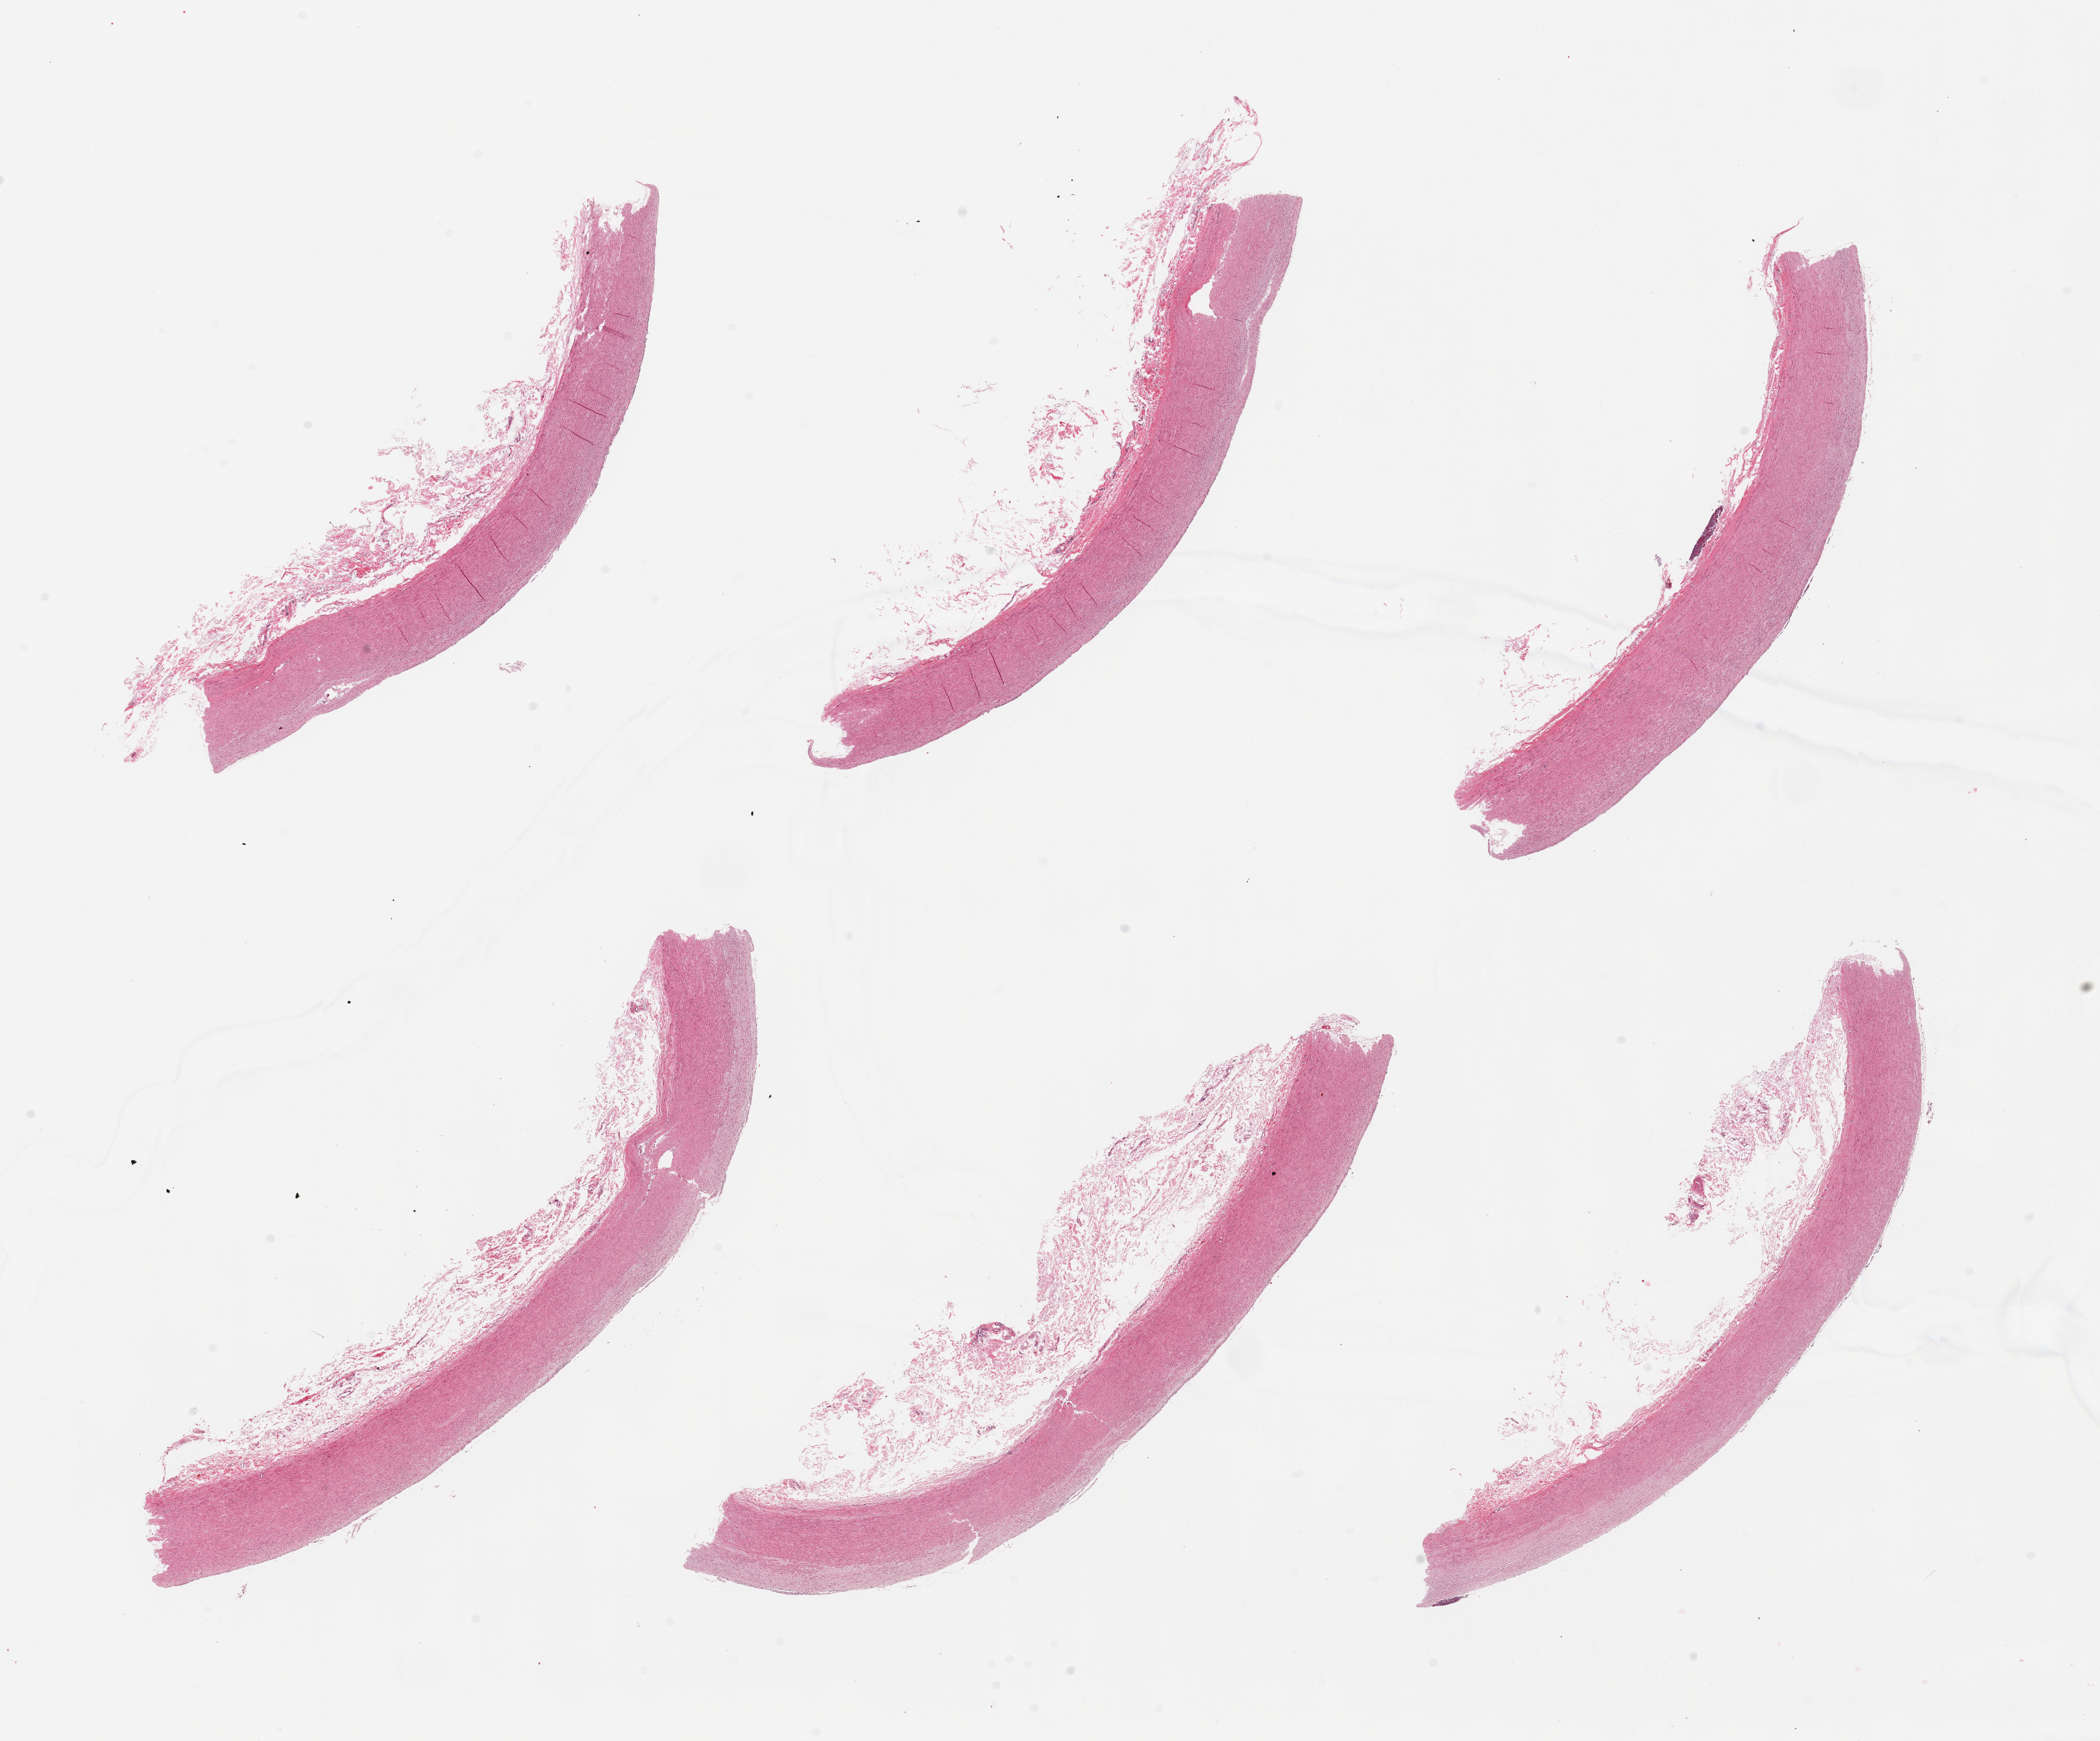
Whole-slide image, hematoxylin and eosin (H&E) stain, brightfield — a low-resolution overview of the entire scanned area, about 25.6 x 21.2 mm. PAXgene-fixed paraffin-embedded (PFPE) section. Sampled site (target tissue): aorta. Tissue donor sample. Female donor.
• reviewer comment on this tissue sample: 6 pieces; includes small detached contaminating fragments of spleen